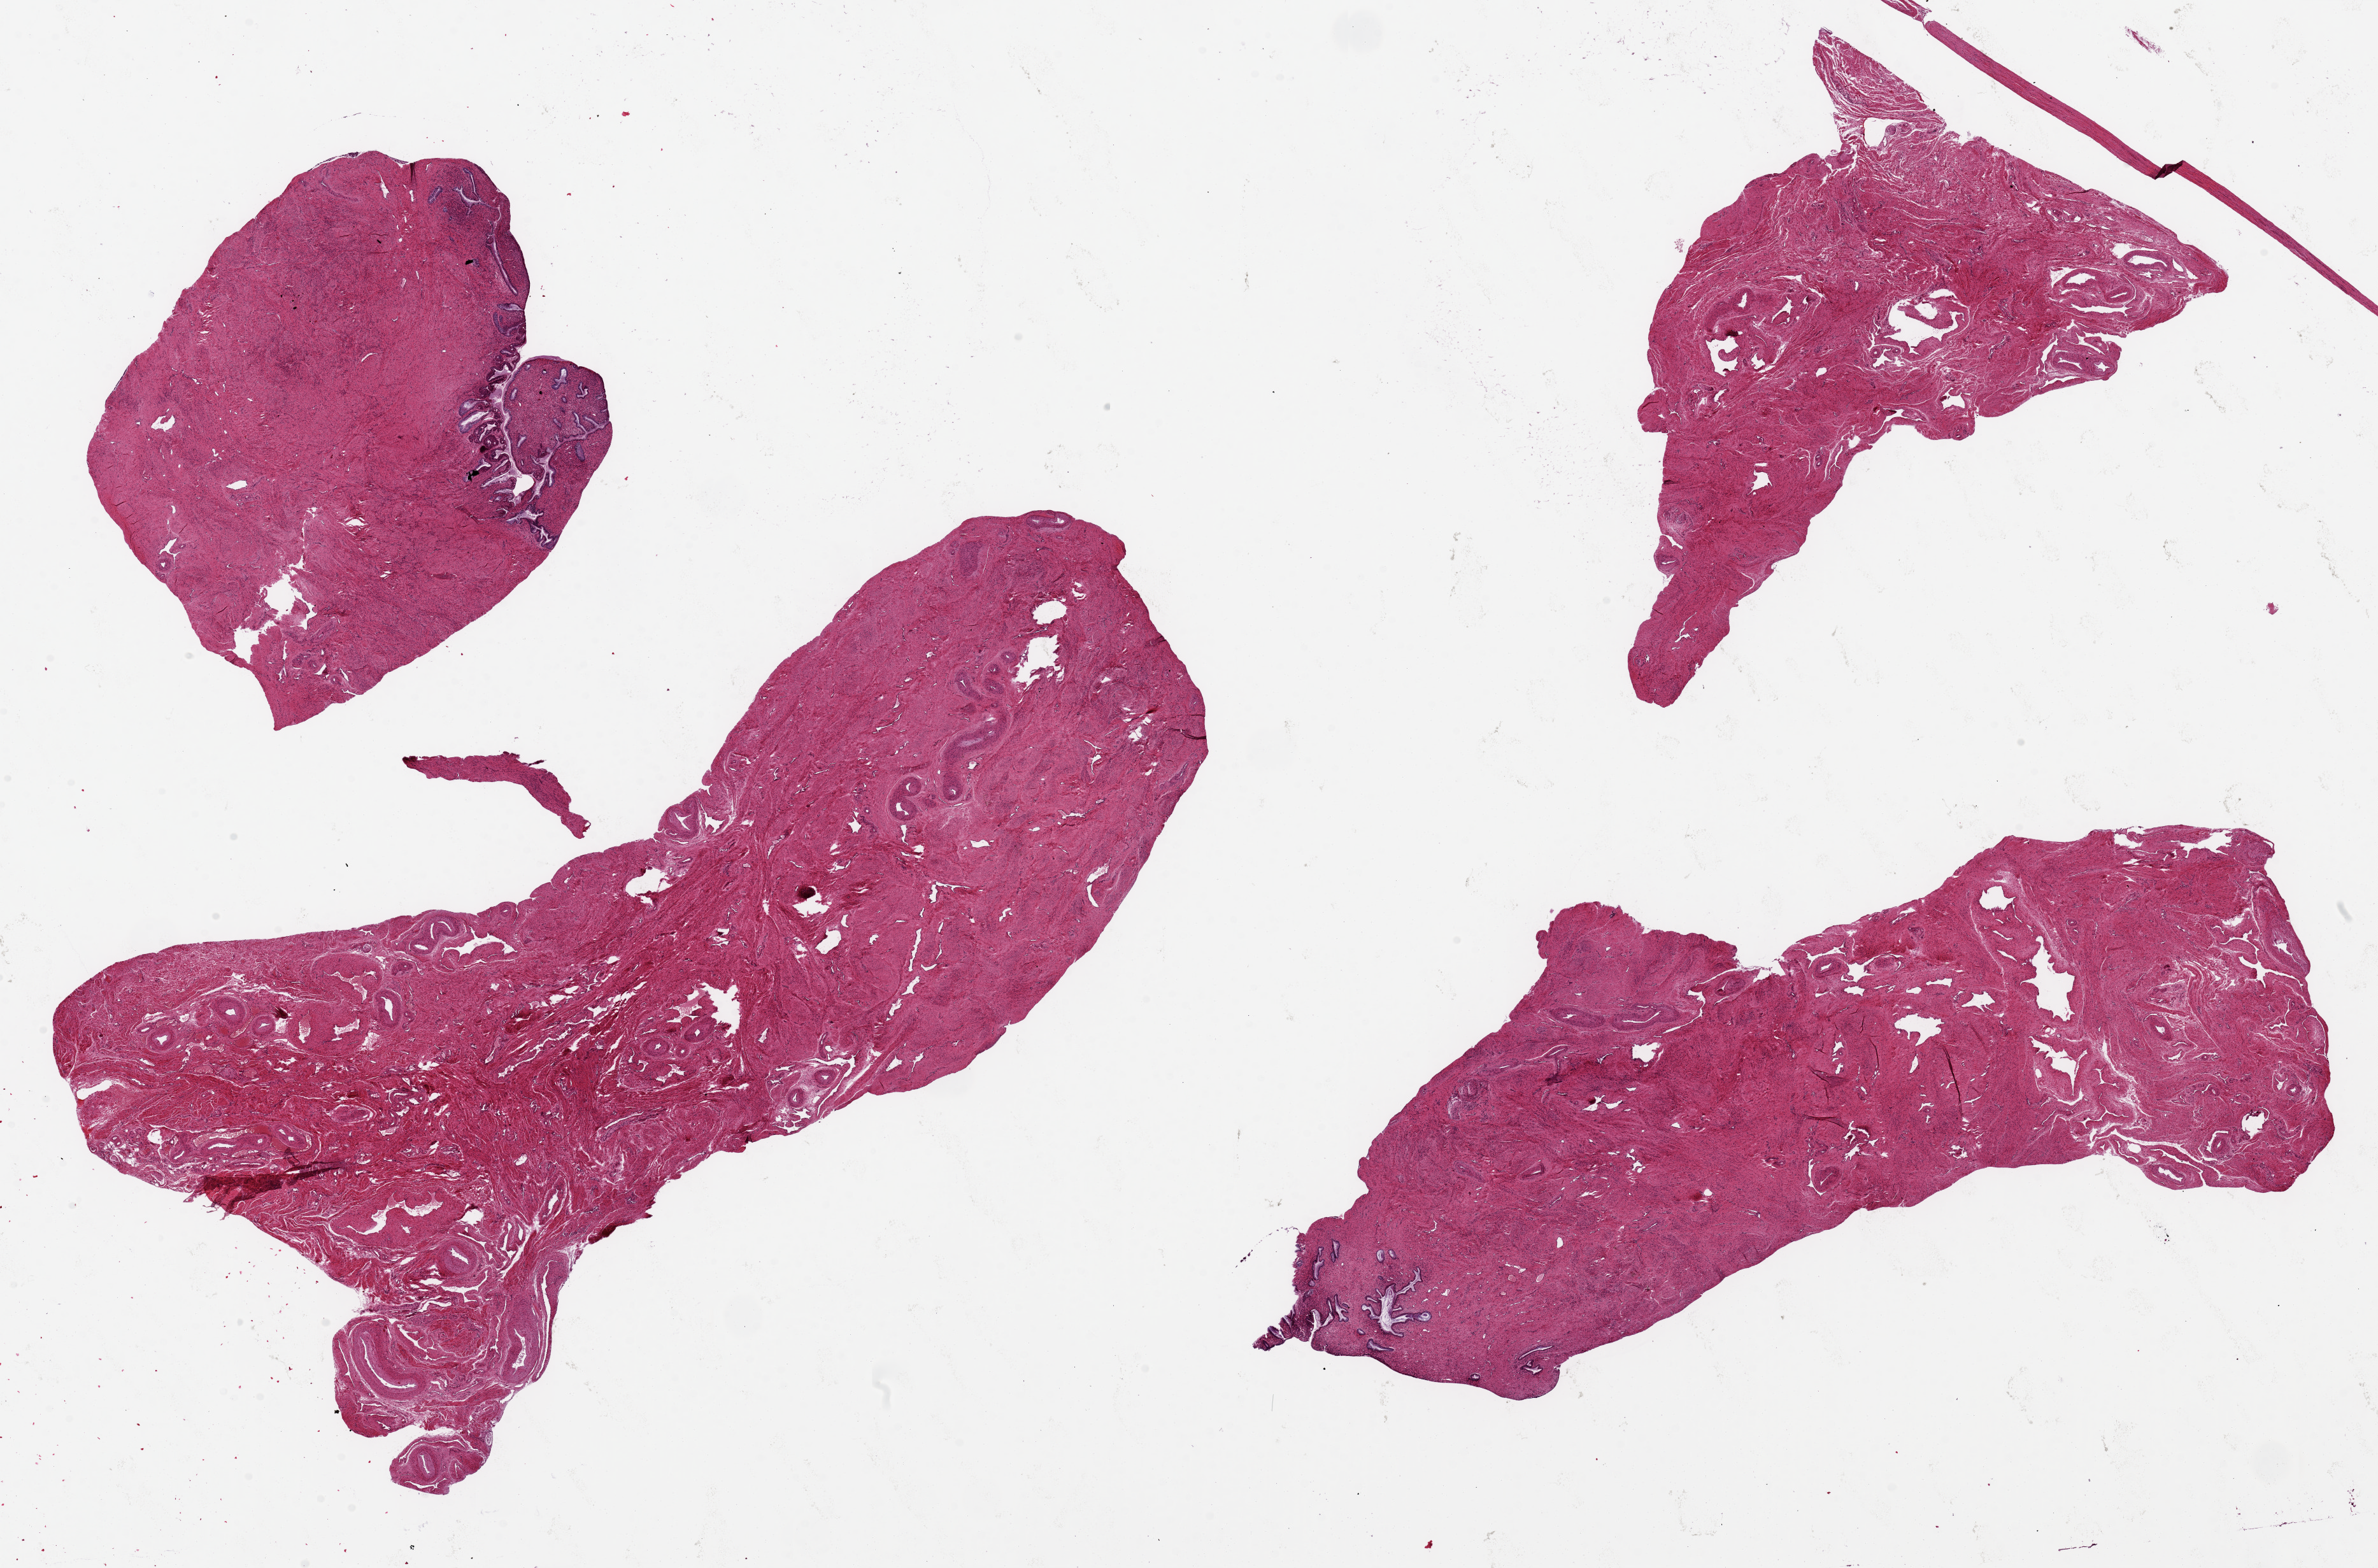
Digitized haematoxylin and eosin-stained section, low-resolution overview of the scanned area, about 29.5 x 19.5 mm (slide scanned at 20x); PAXgene-fixed, paraffin-embedded tissue; target tissue: endocervix; tissue donor sample.
• reviewer comment on this tissue sample: 4 pieces ~10x6mm a few foci of endocervical glands well preserved, up to ~1.5mm d